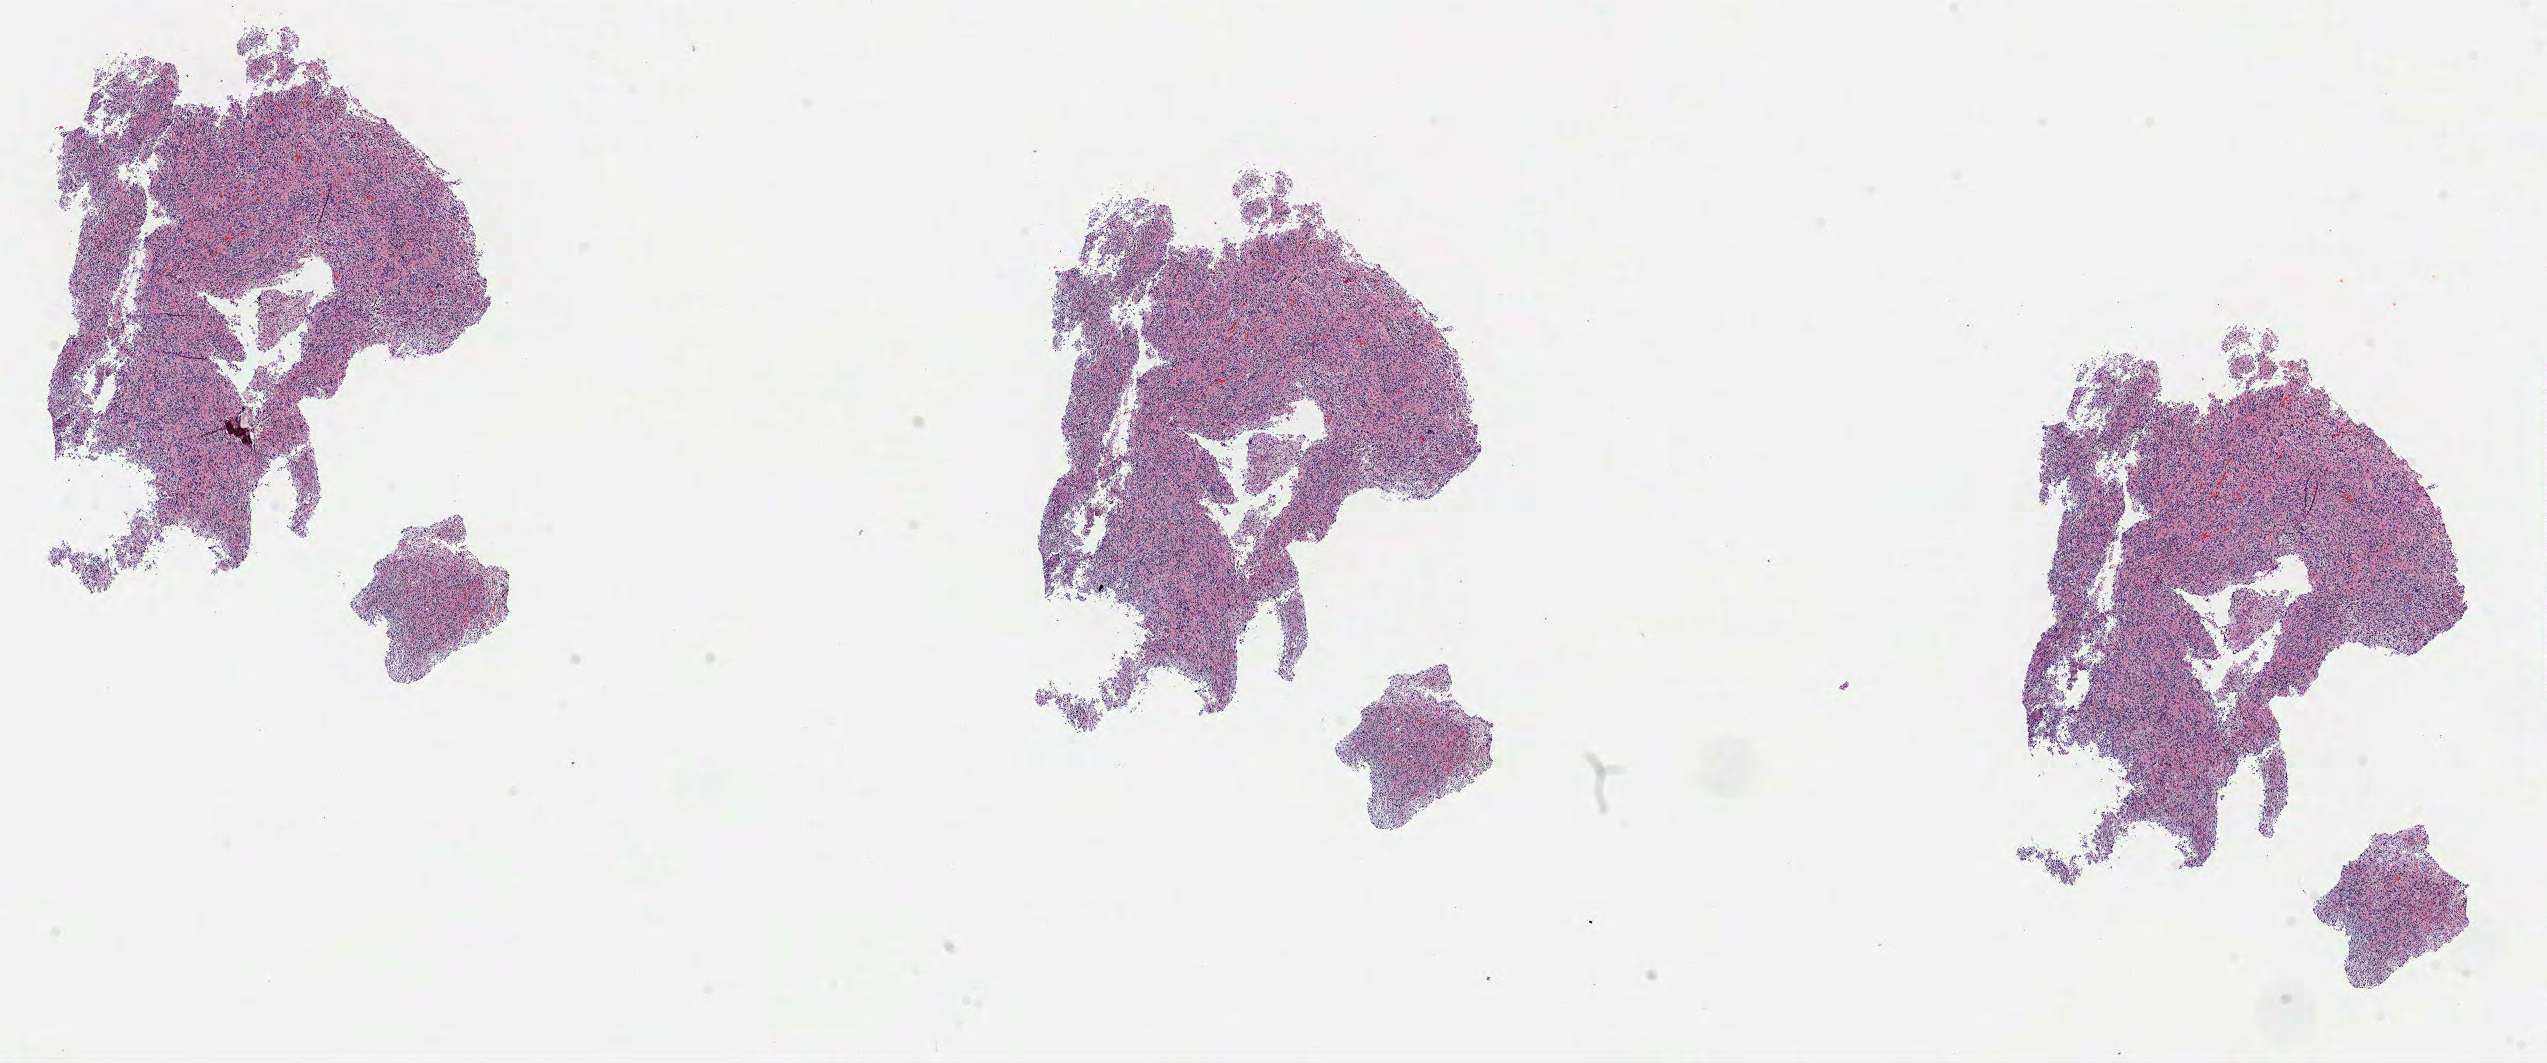
Digitized H&E tissue section (whole slide), whole scanned area (about 20.5 x 8.6 mm, slide scanned at 40x) shown as a low-resolution overview; formalin-fixed paraffin-embedded (FFPE) diagnostic section; brain, primary tumour sample. Female, age 45 years at initial diagnosis.
* diagnosis: Glioblastoma